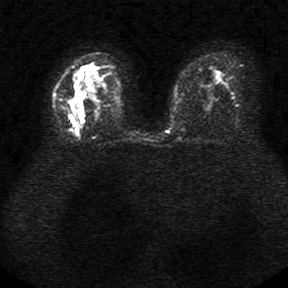
Breast MRI, one axial slice. Slice 19 of 34 in the series (ordered by position). Diffusion-weighted series; image 2 of 4 stored at this slice position (different b-values; order by instance number). 1.5 T. 5 mm slice thickness. 288 × 288 image matrix, field of view 340 × 340 mm. Female patient.
Structures marked on this image (outlined manually by an expert reader):
- tumour on diffusion-weighted imaging: bounding box <75,64,98,114> (left, top, right, bottom; pixels)